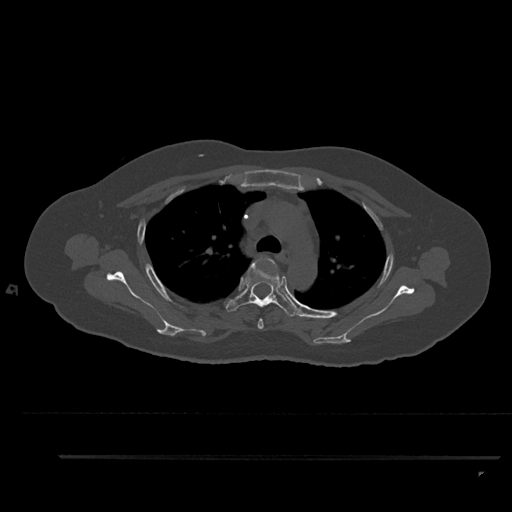
CT including the spine, one axial slice; position 654 of 797 along the scan axis; reconstruction kernel Br40s/3; bone window (W 1800 / L 400 HU); 512 × 512 image matrix, field of view 408 × 408 mm. Female patient, age 44 years. Case-level facts recorded for this patient, not image findings: primary cancer: renal; vertebrae with lytic lesions (as recorded): L1.
Structures marked on this image (semi-automatically segmented with operator editing):
- T3 vertebra: bounding box [x1, y1, x2, y2] px = [257, 259, 276, 329]
- T4 vertebra: [226, 260, 297, 317]